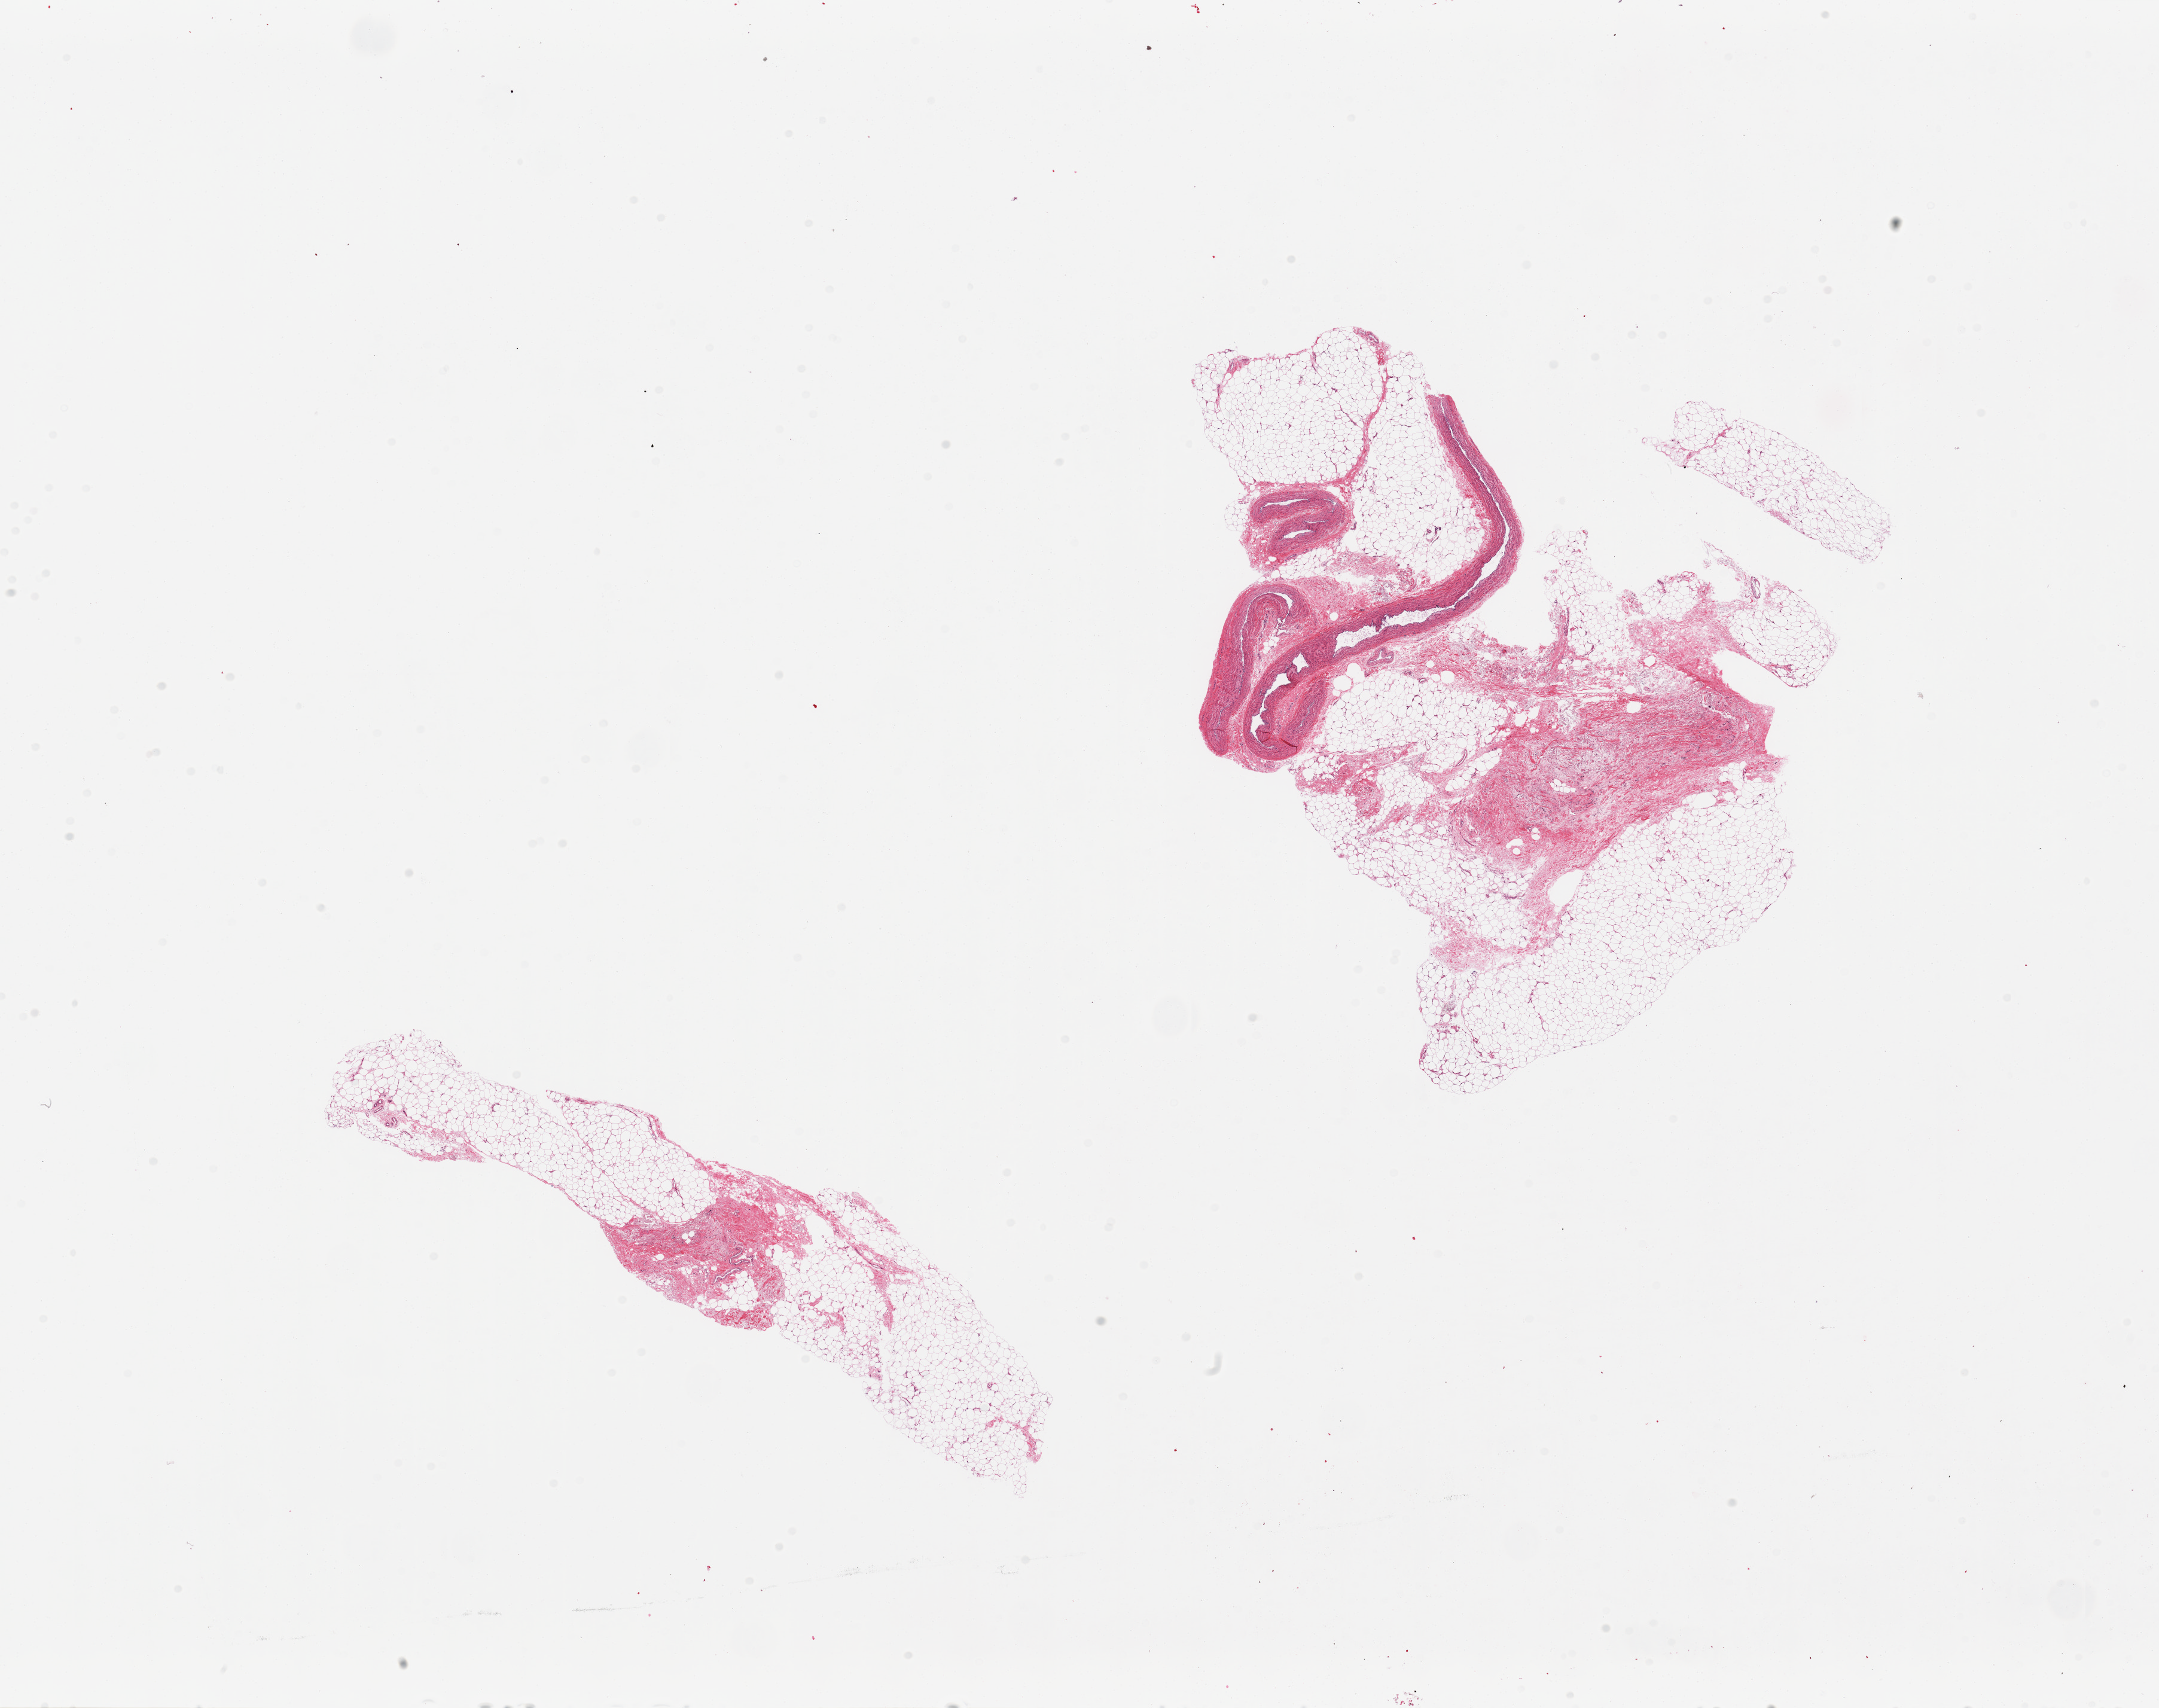
H&E whole-slide image, brightfield — low-resolution overview of the scanned area, about 28.5 x 22.6 mm; PAXgene-fixed, paraffin-embedded tissue; sampled site (target tissue): adipose tissue; donor tissue sample.
Pathologist's review note for this sample: 2 pieces; large blood vessels and fibrous stroma occupy 60%.